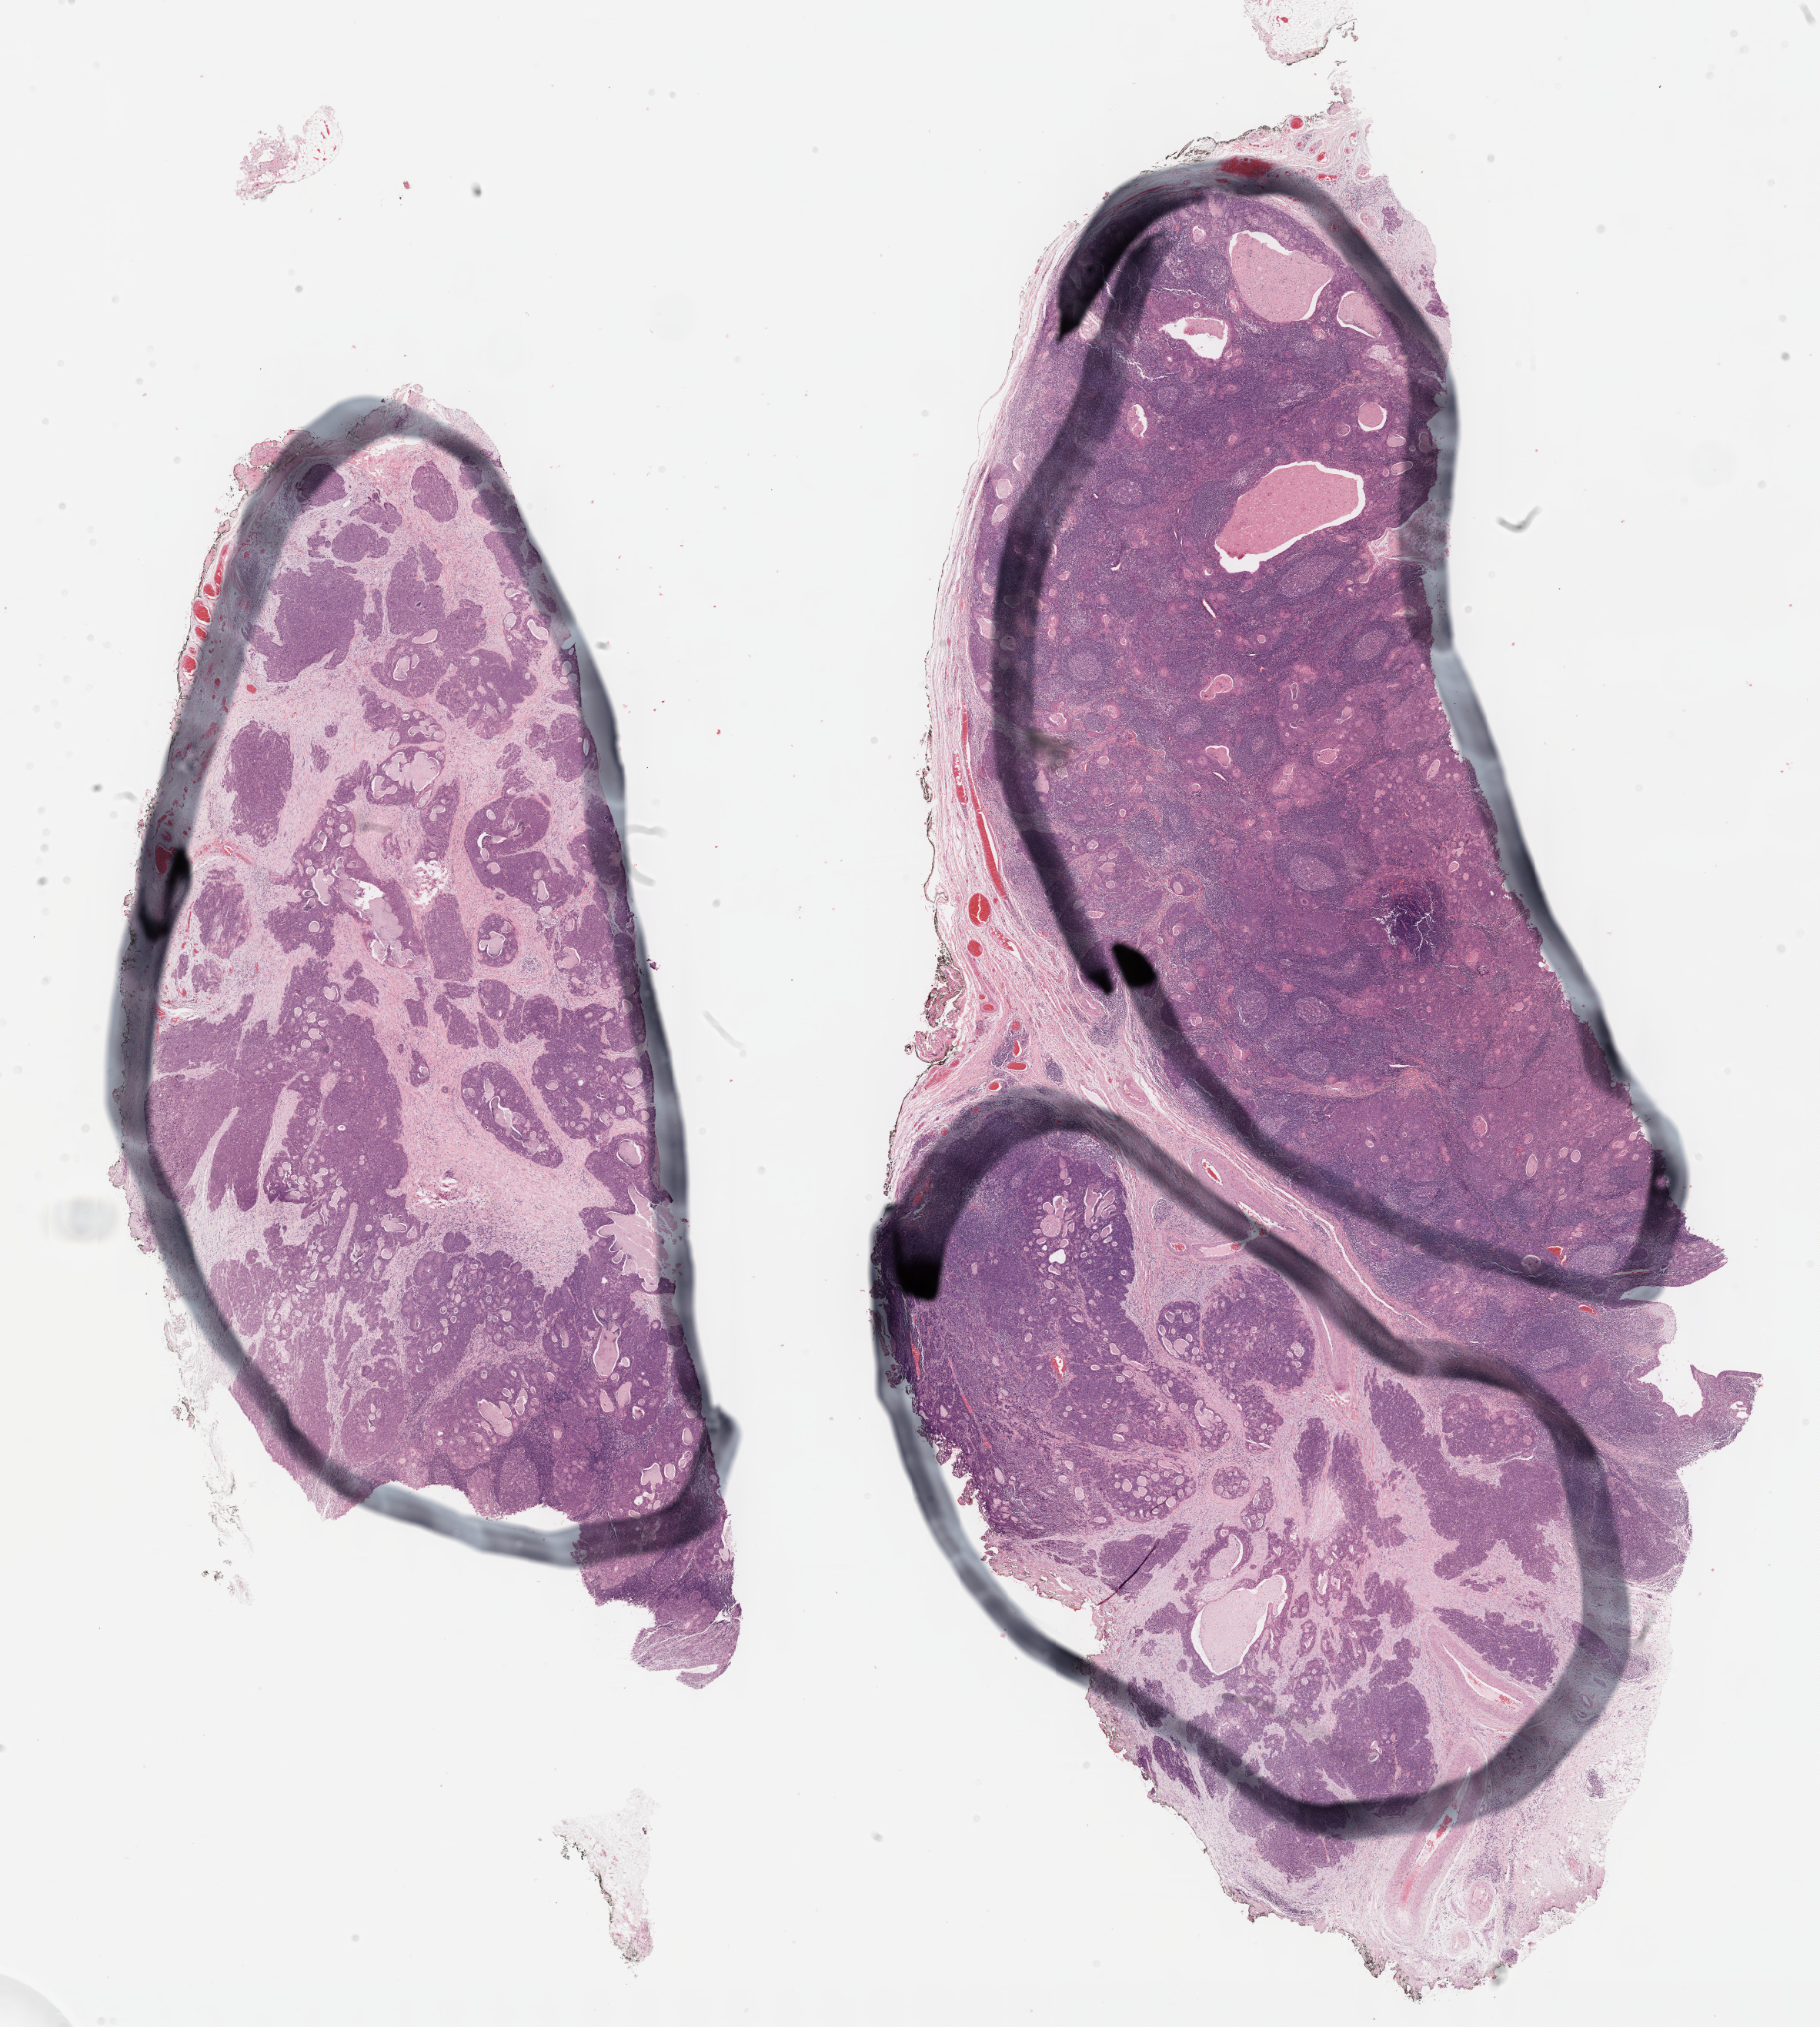
Whole-slide histology image, H&E-stained — a low-resolution overview of the entire scanned area, about 19.1 x 21.3 mm (acquisition: 40x scan). Formalin-fixed paraffin-embedded (FFPE) diagnostic section. Sample: primary tumour, head and neck. Male patient; age at initial diagnosis 58 years. Histologic grade: G4 (undifferentiated).
Pathologic diagnosis: Squamous cell carcinoma, NOS (base of tongue, NOS). Laterality: right.